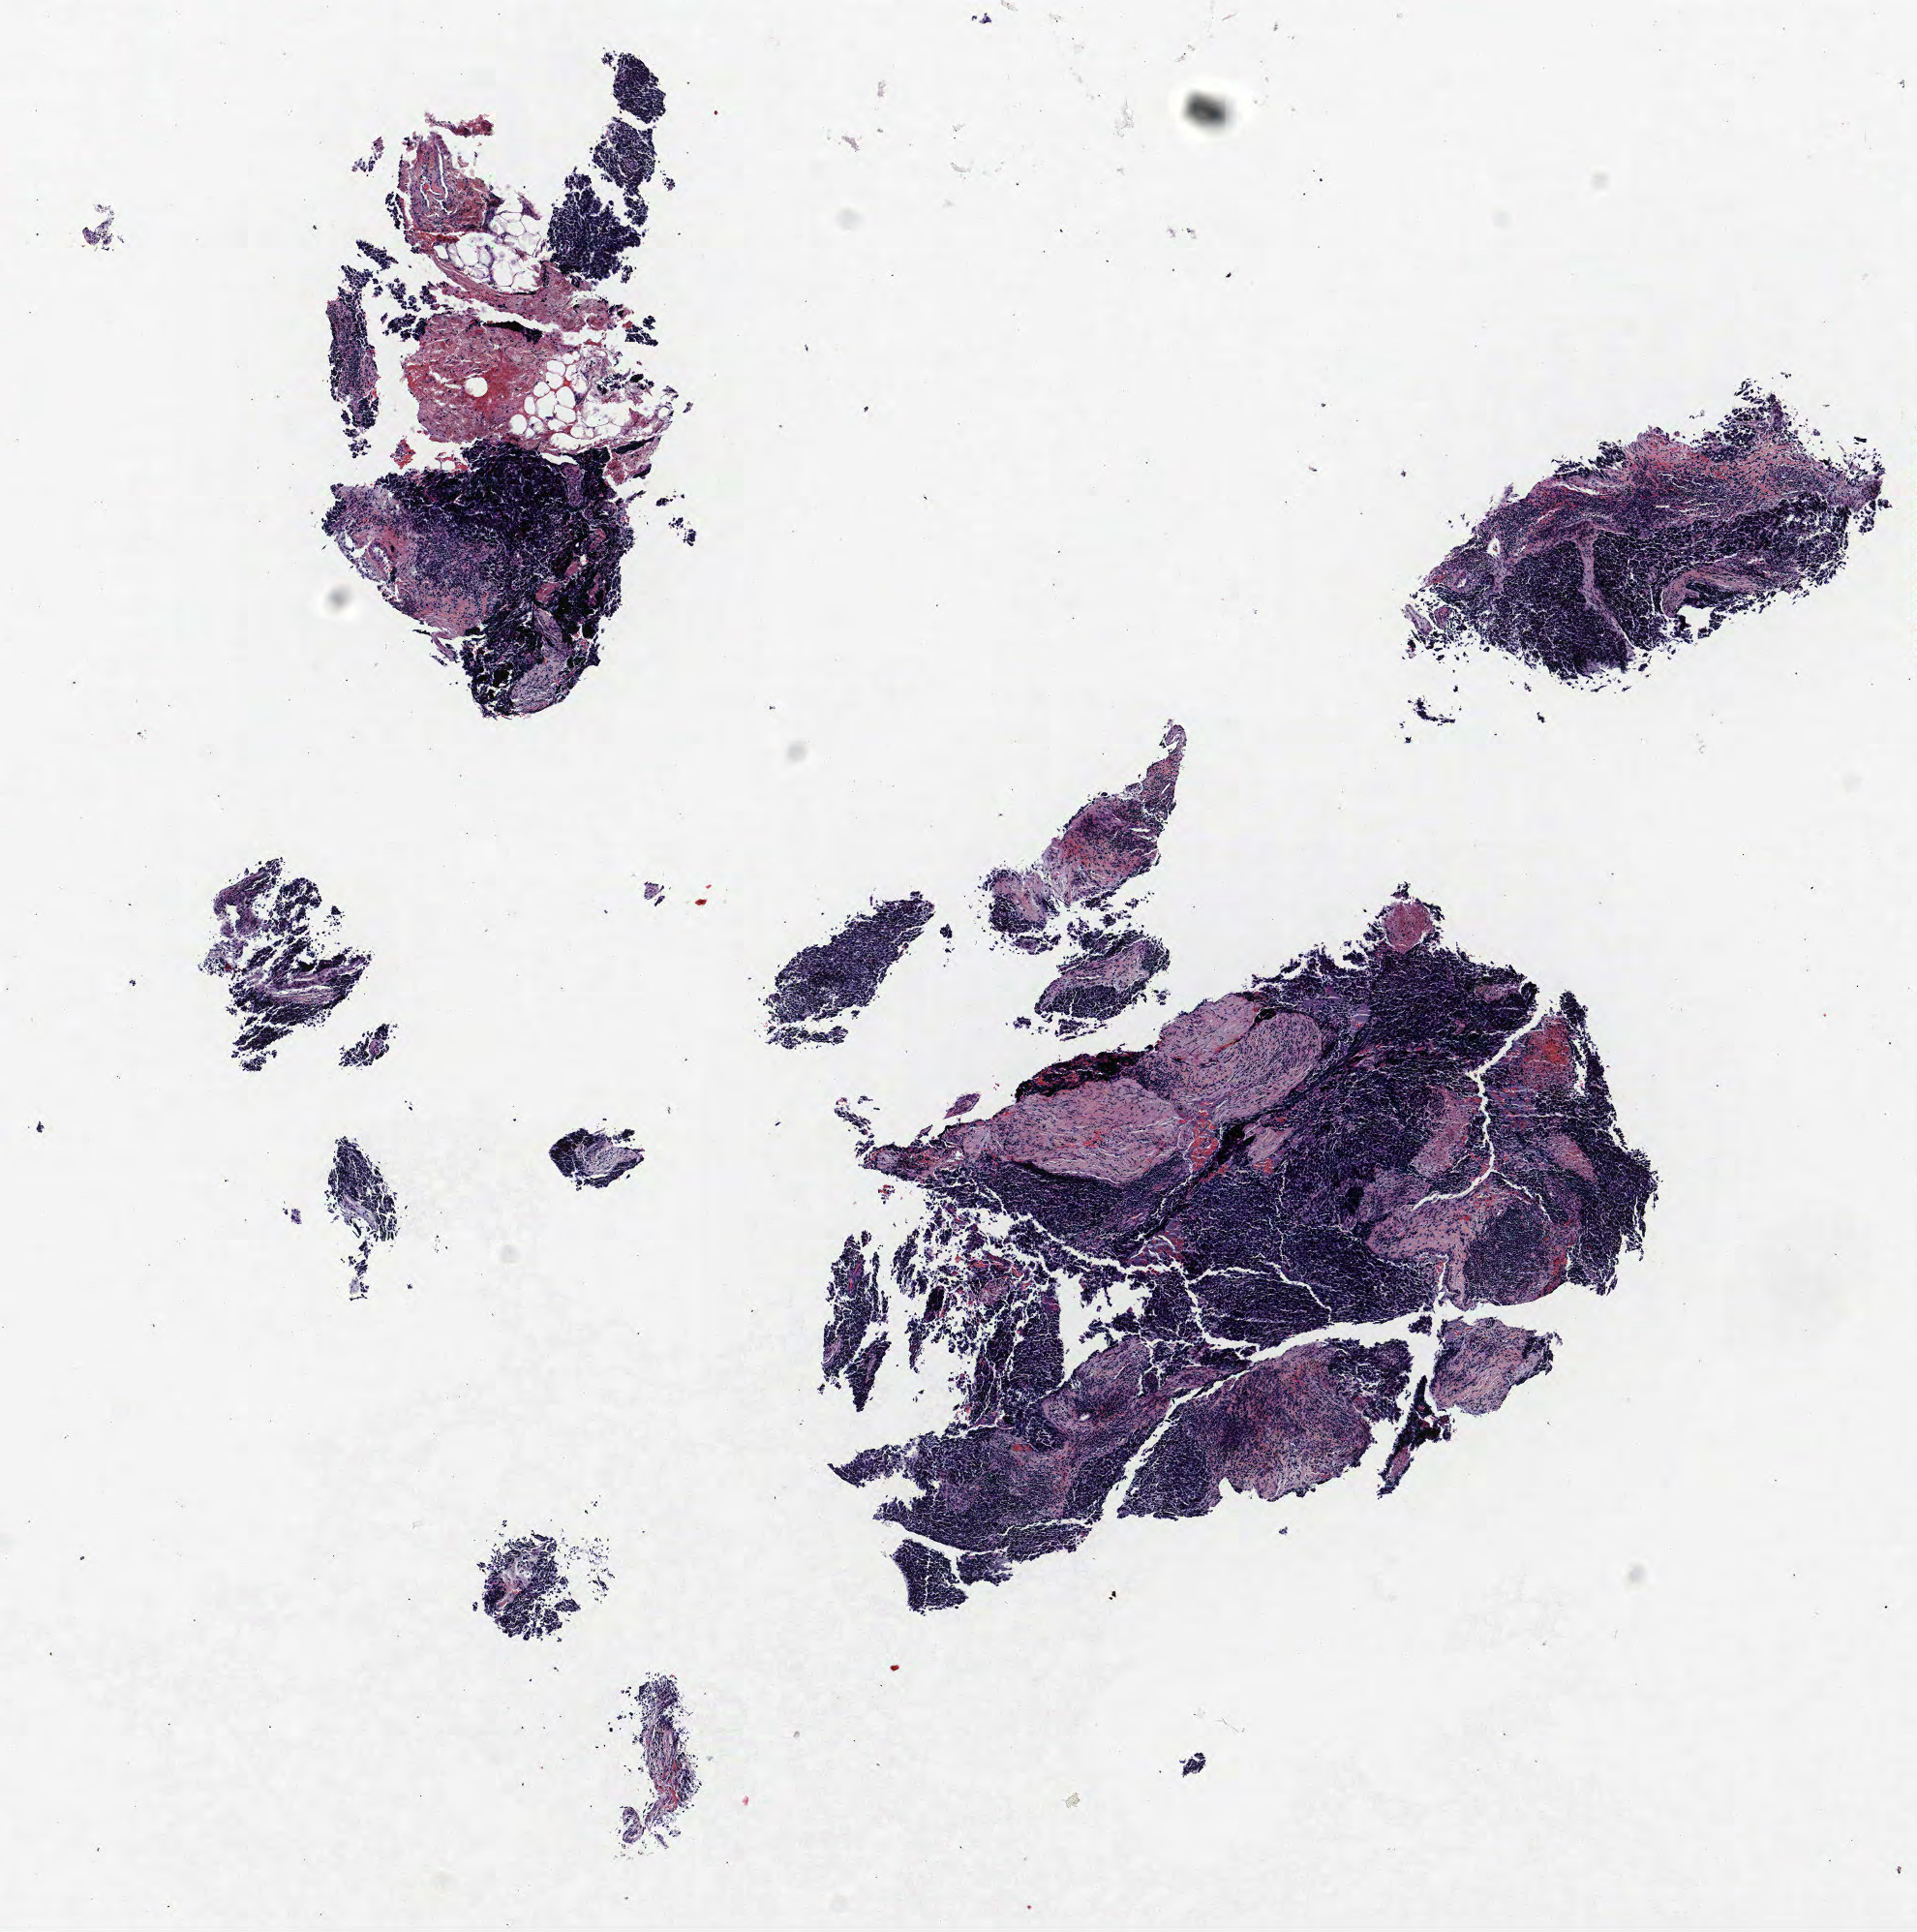
Whole-slide histology image, H&E — whole scanned area (about 7.9 x 8.0 mm, from a 40x scan) shown as a low-resolution overview. FFPE section. Lung. Male patient, aged 72 at enrolment. Former smoker at enrolment. Grade: cannot be assessed (GX).
Stage (AJCC 6th edition): IV. ICD-O-3 topography: upper lobe of lung (C34.1). Primary tumour location (clinical record): right upper lobe. Tumour size (pathology): 7 mm. Participant's lung-cancer diagnosis: Small cell carcinoma, NOS.